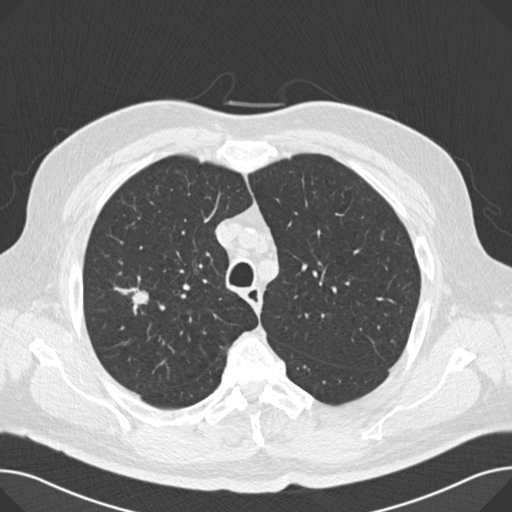
Low-dose screening chest CT, axial slice. Second screening round (one year after baseline). Lung window (W 1500 / L -600 HU). 2 mm slice thickness. 120 kVp. Slice 42 of 166 in the series. 512 × 512 image matrix. Male, age 67 years at enrolment. Current smoker at enrolment.
- Lesion marked by an expert reader, bounding box (x1, y1, x2, y2) in pixels: (124, 283, 153, 312).
- No non-calcified nodule or mass ≥4 mm was recorded by the screening reader at this exam.